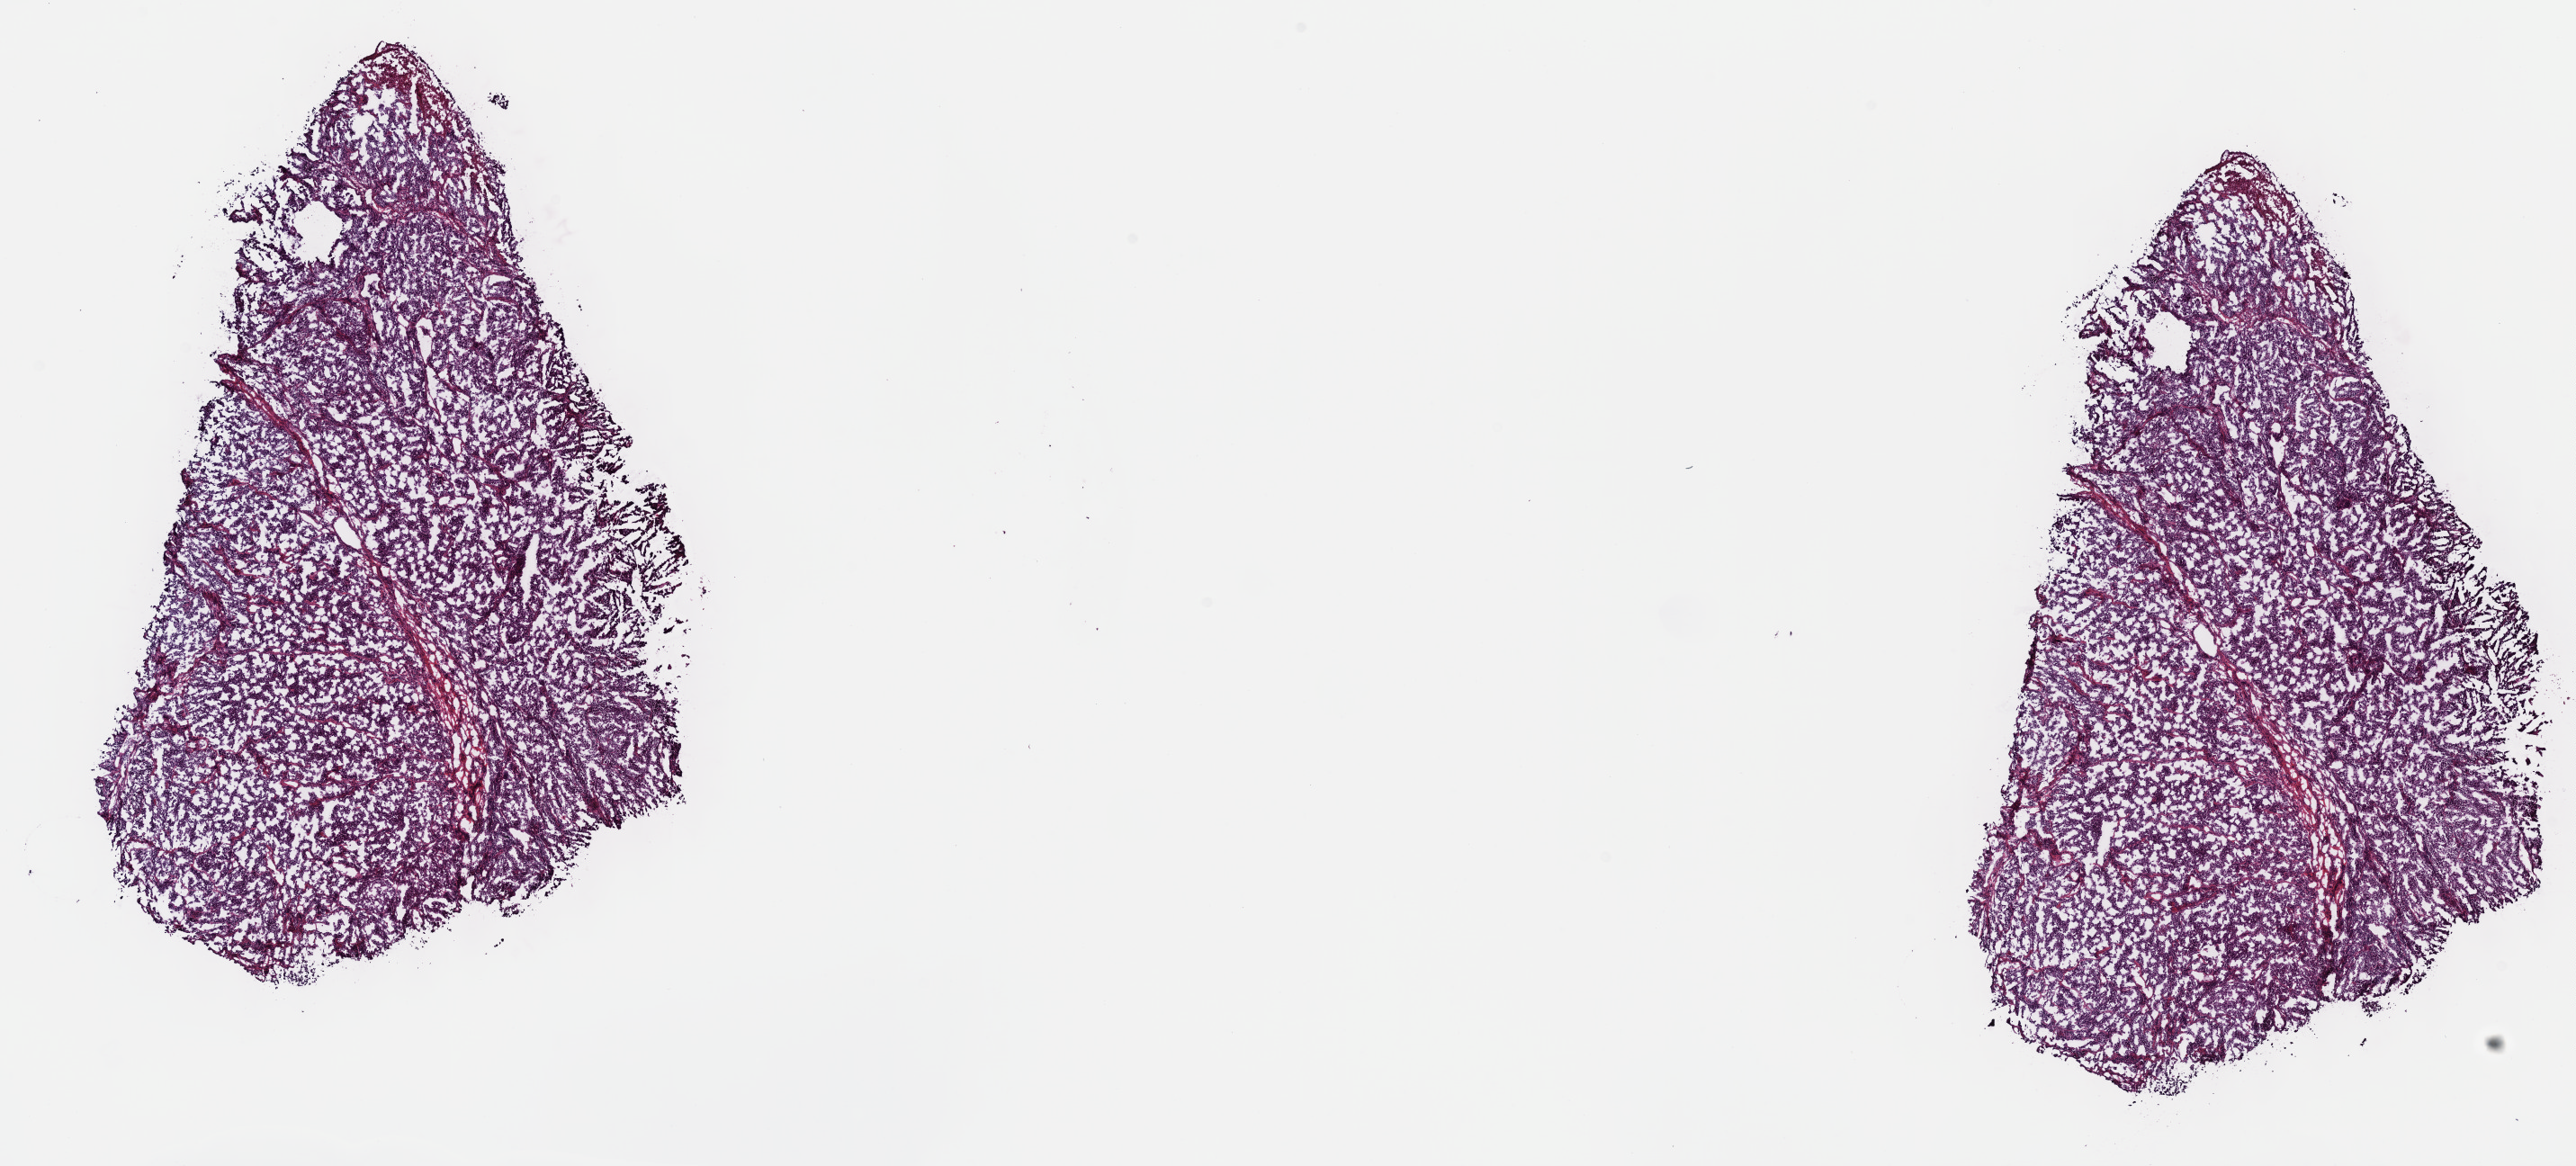
Whole-slide histology image, H&E — low-resolution overview of the scanned area, about 23.2 x 10.5 mm (slide scanned at 40x), frozen section from the top of the tissue portion, metastatic tumour sample, sampled site: connective, subcutaneous and other soft tissues of upper limb and shoulder. Male patient; age at initial diagnosis 73 years. Pathologist review of this section (percent, as recorded): tumour cells 100%, tumour nuclei 80%, normal cells 0%, stromal cells 0%, necrosis 0%. Inflammatory infiltration, as recorded: lymphocyte infiltration 1%, monocyte infiltration 0%, neutrophil infiltration 0%.
This section: metastatic tumour tissue. Patient diagnosis: Malignant melanoma, NOS.